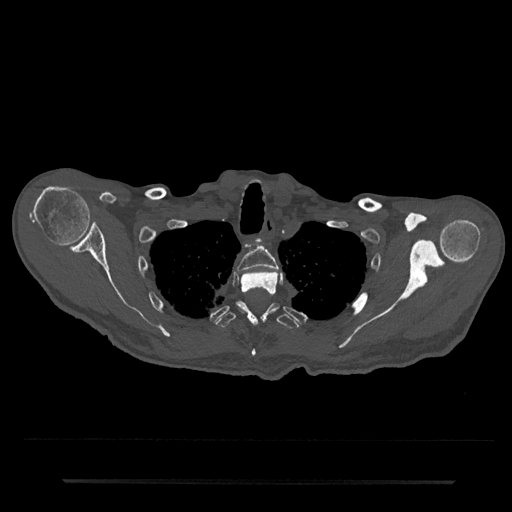
CT including the spine, one axial slice. Slice 652 of 797 in the series (ordered by position). Reconstruction kernel Br40s/3. 120 kVp. Bone window (W 1800 / L 400 HU). 0.5 mm slice thickness. 512 × 512 image matrix, field of view 427 × 427 mm. Male patient, age 74 years. From the clinical record (not read from this slice): primary cancer: prostate.
Annotated regions visible in this slice (semi-automatically segmented with operator editing):
- T2 vertebra: bounding box [x1, y1, x2, y2] px = [237, 247, 278, 272]
- T3 vertebra: [240, 271, 278, 356]
- T4 vertebra: [216, 301, 300, 329]